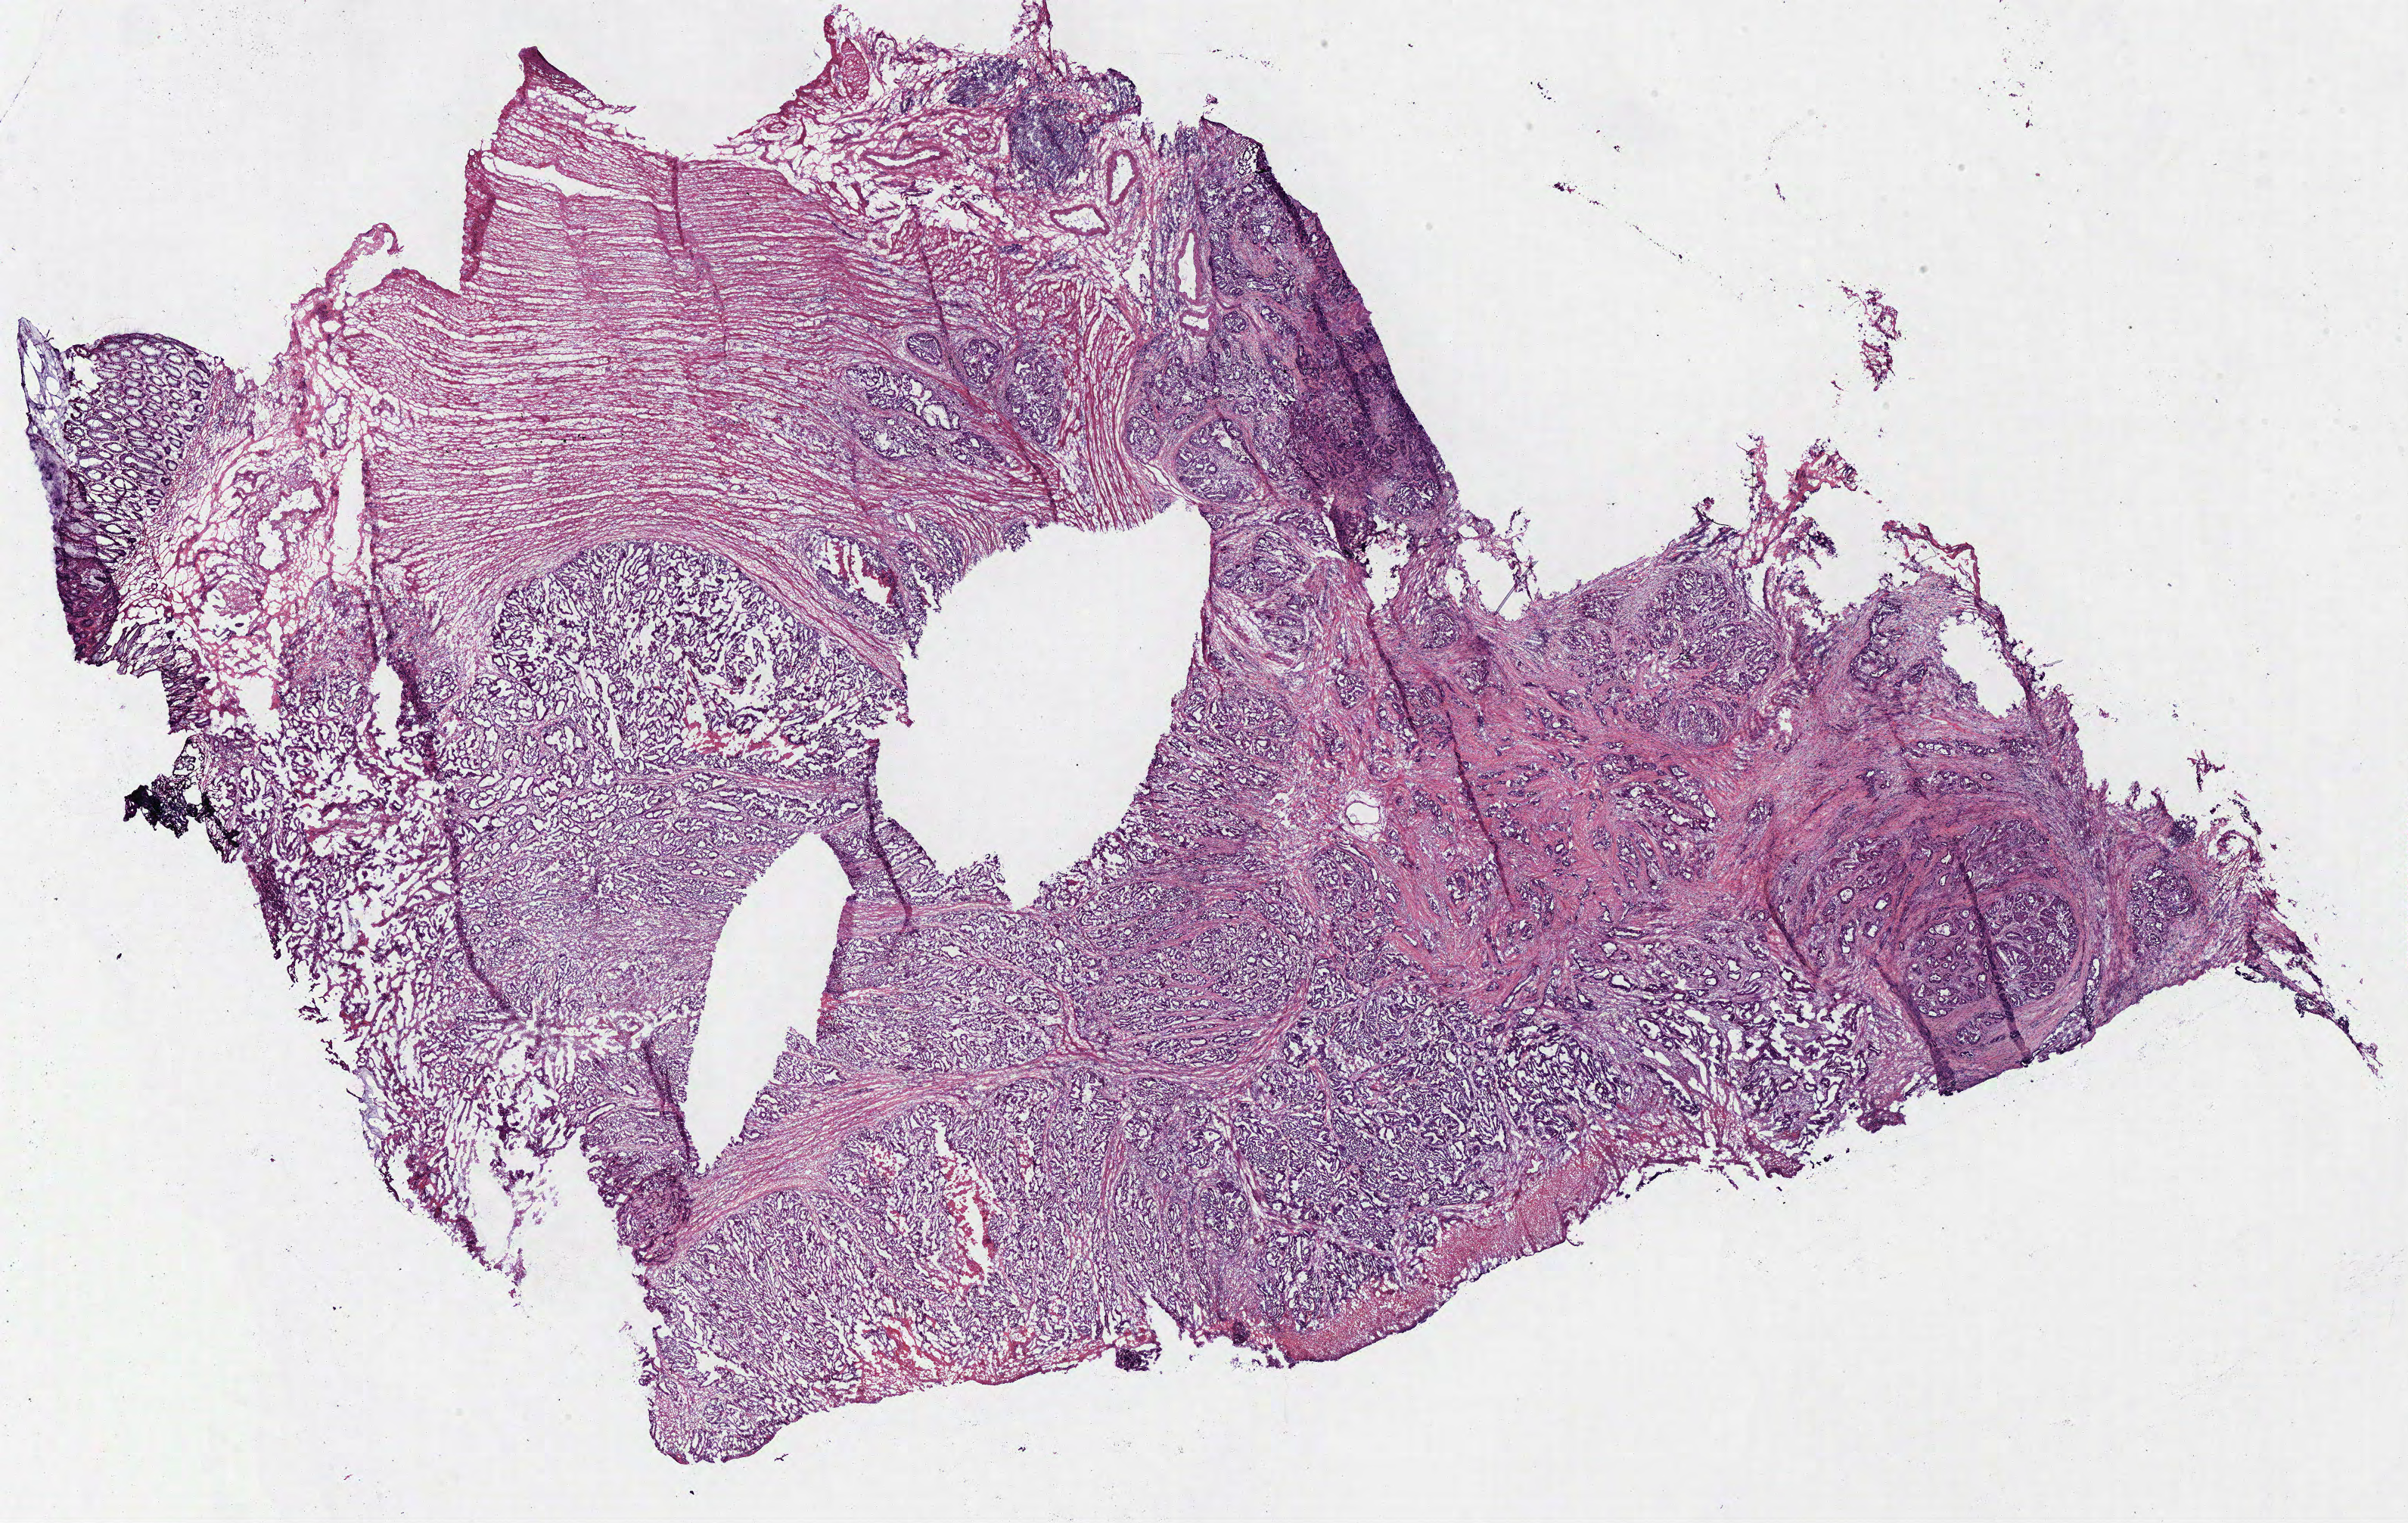
Whole-slide histology image, Hematoxylin and eosin (H&E) stained — a low-resolution overview of the entire scanned area, about 25.1 x 15.9 mm. Frozen section. Primary tumour sample from the rectum. Male, age 70 years at initial diagnosis. Slide review estimates, as recorded: tumour cells 80%, tumour nuclei 80%, normal cells 15%, necrosis 5%. Inflammatory infiltration, as recorded: lymphocyte infiltration 8%, monocyte infiltration 1%, neutrophil infiltration 2%.
Diagnosis: Adenocarcinoma, NOS (connective, subcutaneous and other soft tissues of abdomen). AJCC pathologic stage: IIIC. Lymph nodes positive (case pathology): 12 of 12 examined.